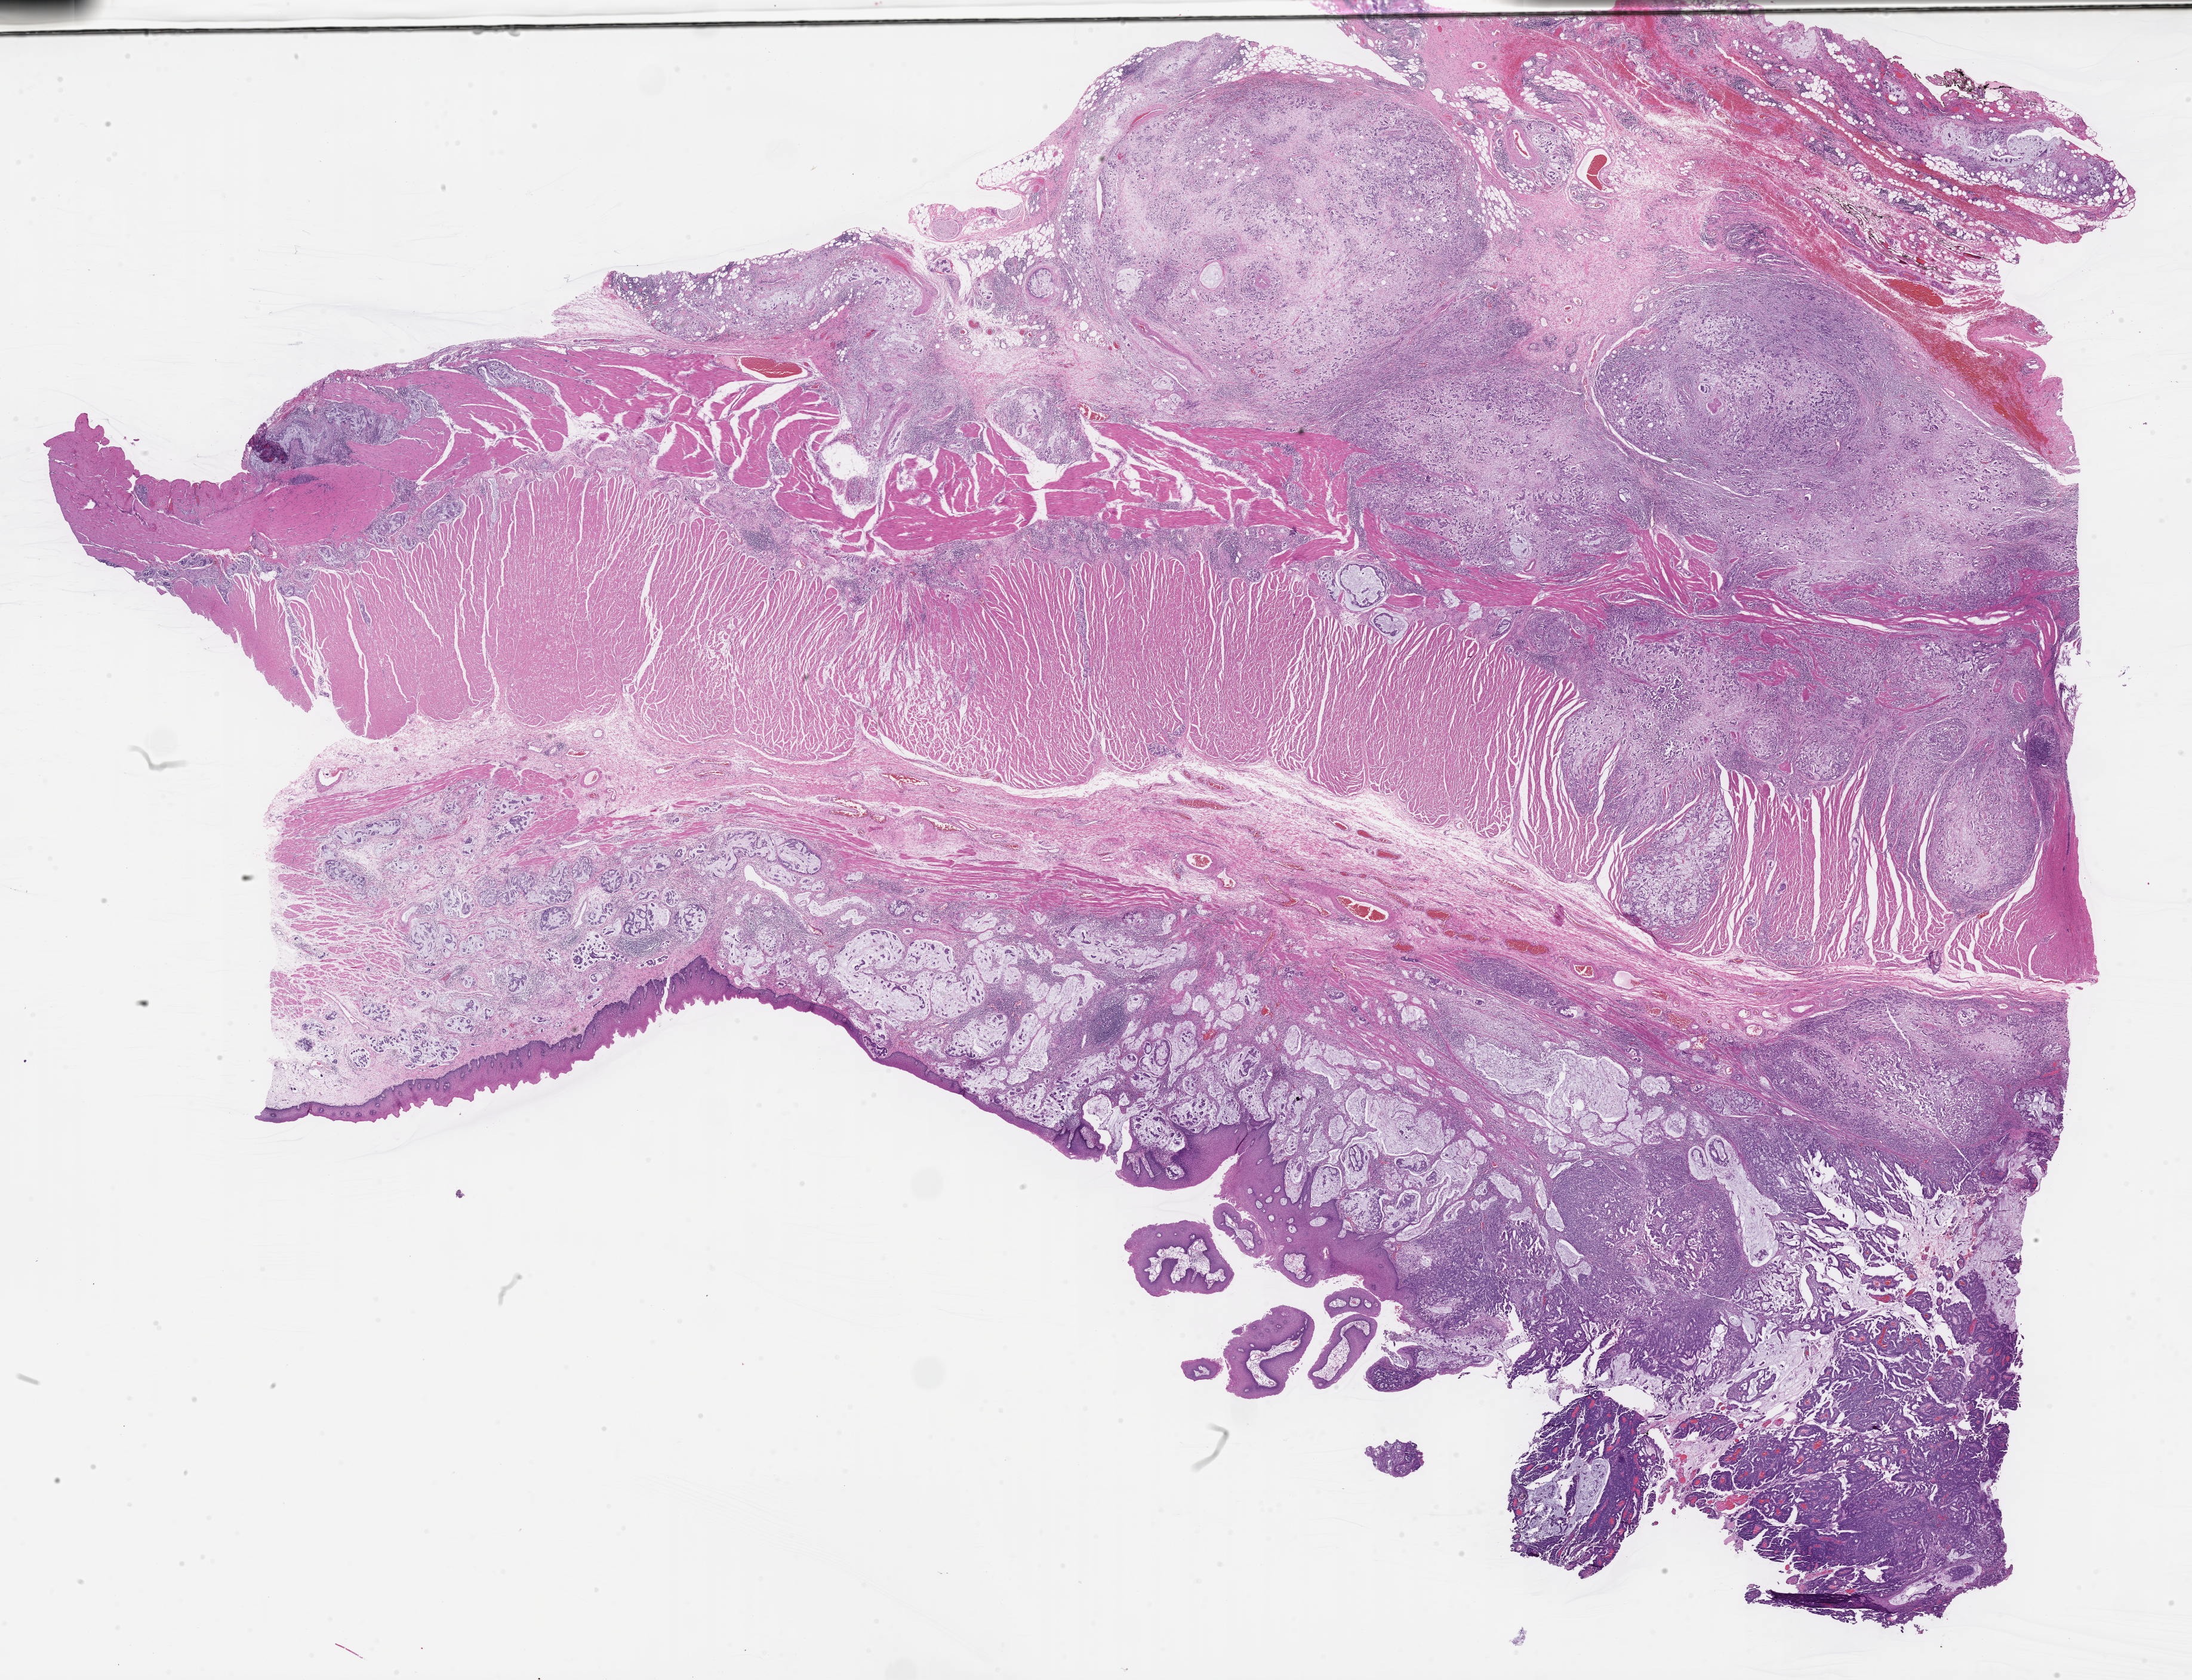
Haematoxylin and eosin whole-slide image, a low-resolution overview of the entire scanned area, about 29.6 x 22.7 mm, formalin-fixed, paraffin-embedded (FFPE) tissue, primary tumor. Patient: male, age at initial diagnosis 42 years. Tumor grade: G3 (poorly differentiated). Slide review estimates, as recorded: tumor cells 75%, tumor nuclei 75%, stromal cells 22%, necrosis 1%, normal cells 2%. Infiltration values recorded for this section: lymphocyte infiltration 7%, monocyte infiltration 4%, neutrophil infiltration 5%.
Diagnosis: Adenocarcinoma, NOS. AJCC pathologic stage: Stage IIIC.